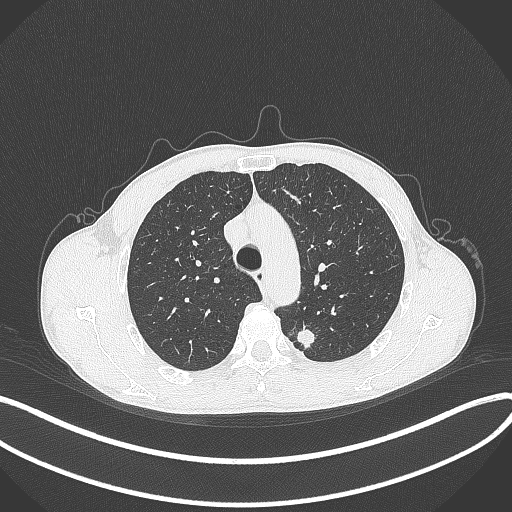
Chest CT, one axial slice. Slice 297 of 429 in the series (ordered by position). Reconstruction kernel B70f. 120 kVp. Lung window (W 1500 / L -600 HU). 1 mm slice thickness. 512 × 512 image matrix, field of view 400 × 400 mm. Male patient, age 51 years. Case-level facts recorded for this patient, not image findings: clinical TNM (as recorded): T2a N1 M1.
Structures marked on this image (bounding box drawn by a radiologist):
- lung tumour (recorded histology: adenocarcinoma): bounding box [x1, y1, x2, y2] px = [294, 325, 321, 357]